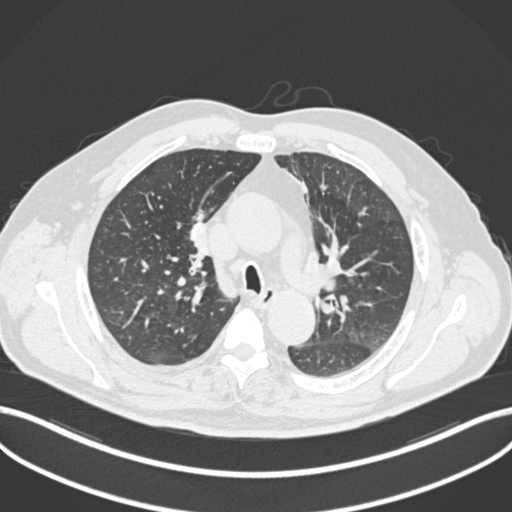
Chest CT, one axial slice. Position 131 of 255 along the scan axis. 120 kVp. Lung window (W 1500 / L -600 HU). 1 mm slice thickness. 512 × 512 image matrix. Patient: male, 60 years. From the clinical record (not read from this slice): clinical TNM (as recorded): T1b N1 M0.
Outlined on this slice (rectangle marked by the reading radiologist):
- lung tumour (recorded histology: squamous cell carcinoma): bounding box (x1, y1, x2, y2) in pixels: (183, 204, 218, 281)